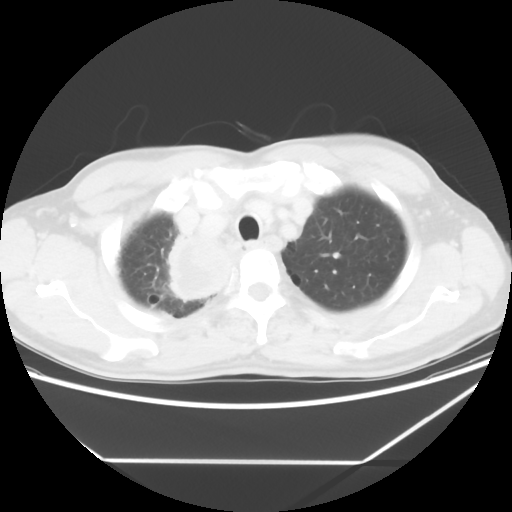
Chest CT, one axial slice; position 51 of 60 along the scan axis; reconstruction kernel STANDARD; lung window (W 1500 / L -600 HU); 5 mm slice thickness; 512 × 512 image matrix, field of view 367 × 367 mm. Male patient, age 58 years. From the clinical record (not read from this slice): clinical TNM (as recorded): T2 N2 M0.
Outlined on this slice (rectangle marked by the reading radiologist):
- lung tumour (recorded histology: squamous cell carcinoma): bounding box <163,233,235,307> (left, top, right, bottom; pixels)